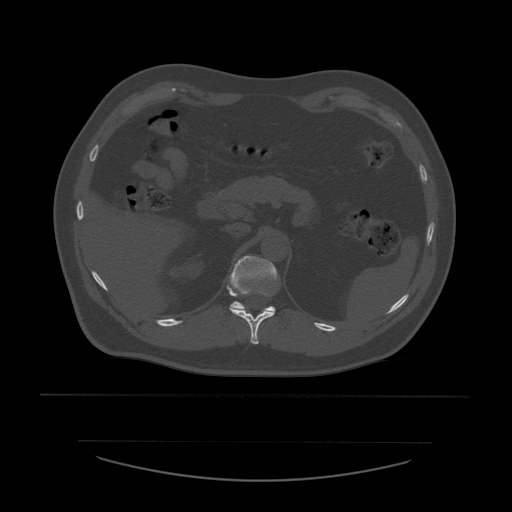
CT including the spine, one axial slice; slice 265 of 532 in the series (ordered by position); reconstruction kernel STANDARD; 120 kVp; bone window (W 1800 / L 400 HU); 1.25 mm slice thickness; 512 × 512 image matrix. Patient age 44 years. From the clinical record (not read from this slice): primary cancer: soft tissue sarcoma.
Structures marked on this image (semi-automatic segmentation, software-assisted and operator-edited):
- T11 vertebra: bounding box [x1, y1, x2, y2] px = [229, 291, 275, 345]
- T12 vertebra: [227, 255, 278, 312]